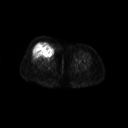
FDG PET of an extremity soft-tissue mass (from a PET/CT study), one axial slice; position 34 of 267 along the scan axis; 3.27 mm slice thickness; 128 × 128 image matrix, field of view 700 × 700 mm. Female patient, age 56 years. Case-level facts recorded for this patient, not image findings: histological type: malignant solitary fibrous tumor; grade: intermediate; site of the primary tumour: right thigh.
Outlined on this slice (expert contour drawn on MRI and transferred to this co-registered scan by the dataset authors):
- gross tumour volume including surrounding oedema: bounding box (x1, y1, x2, y2) in pixels: (33, 41, 55, 59)
- gross tumour volume (mass): (35, 41, 55, 58)